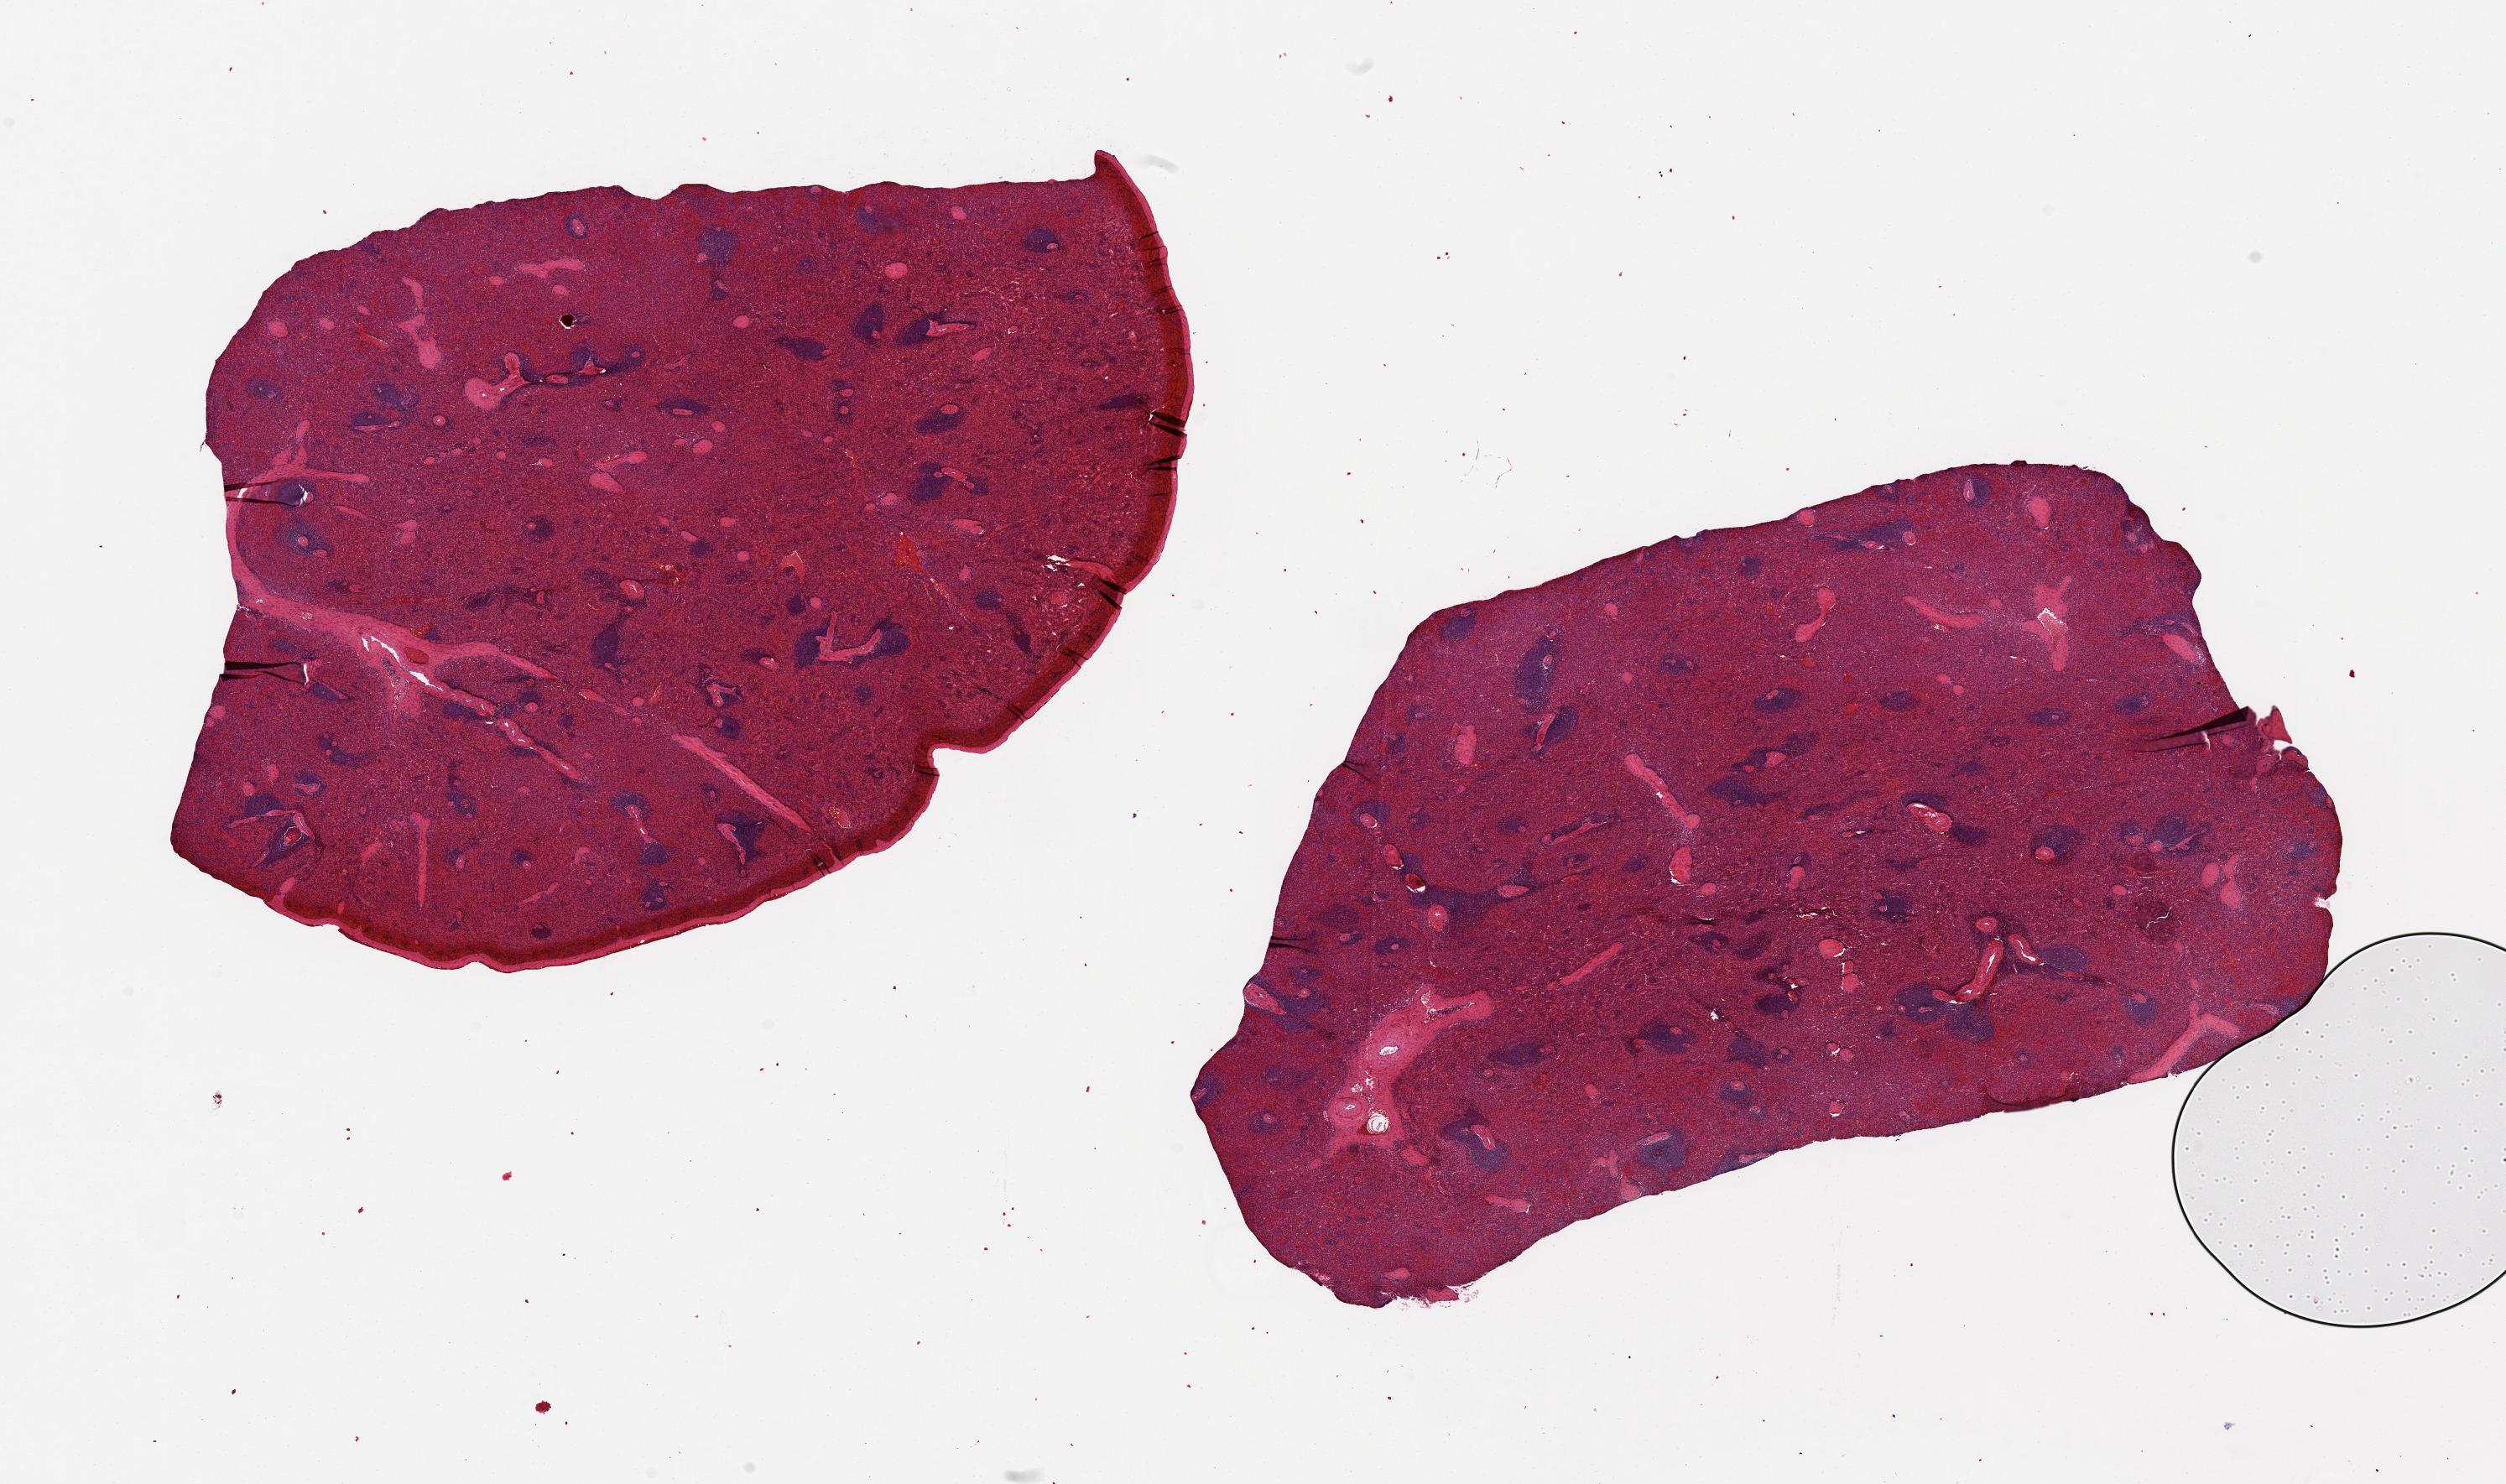
Digitized hematoxylin and eosin (H&E)-stained section — whole scanned area (about 23.6 x 14.0 mm, slide scanned at 20x) shown as a low-resolution overview; PAXgene-fixed paraffin-embedded (PFPE) section; target tissue: spleen; tissue donor sample.
Review note (as recorded): 2 pieces, 10x7 & 11x6 mm; capsule present on one piece (aliquot should be 5 mm beneath capsule).